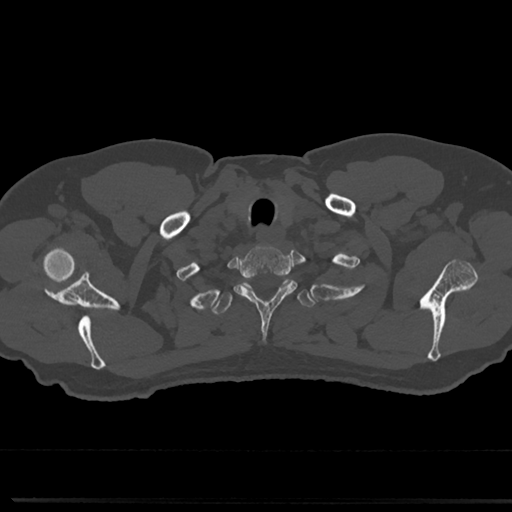
CT including the spine, one axial slice; reconstruction kernel Br40s/3; 120 kVp; bone window (W 1800 / L 400 HU); 512 × 512 image matrix, field of view 355 × 355 mm. Male patient, age 61 years. Case-level facts recorded for this patient, not image findings: primary cancer: prostate.
Outlined on this slice (semi-automatic segmentation, software-assisted and operator-edited):
- T1 vertebra: bounding box [x1, y1, x2, y2] px = [235, 247, 296, 309]
- T2 vertebra: [213, 278, 315, 315]